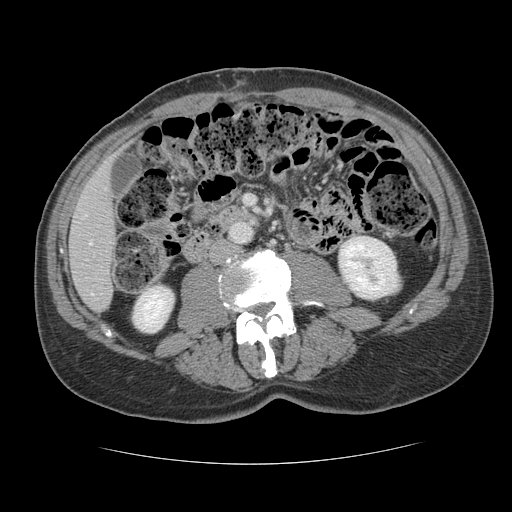
Contrast-enhanced abdominal CT, one axial slice; position 36 of 134 along the scan axis; reconstruction kernel STANDARD; 120 kVp; soft-tissue window (W 400 / L 40 HU); 2.5 mm slice thickness; 512 × 512 image matrix, field of view 377 × 377 mm. Male patient, age 68 years. Case-level facts recorded for this patient, not image findings: diagnosis: colorectal cancer liver metastases, imaged before liver resection.
Structures marked on this image (expert manual segmentation):
- hepatic veins: box from (x=89, y=242) to (x=92, y=245) px
- liver: (x=70, y=166)–(x=116, y=311)
- planned liver remnant (the part of the liver to remain after resection): (x=70, y=165)–(x=116, y=310)
- portal vein (with intrahepatic branches): (x=91, y=293)–(x=93, y=295)